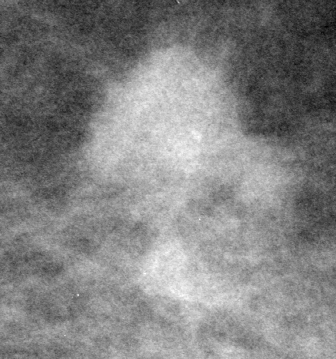
Crop from a digitized film mammogram around one marked abnormality; left breast; CC view.
Finding: mass, shape lobulated, margins microlobulated; BI-RADS assessment category 5; pathology (as recorded): malignant.